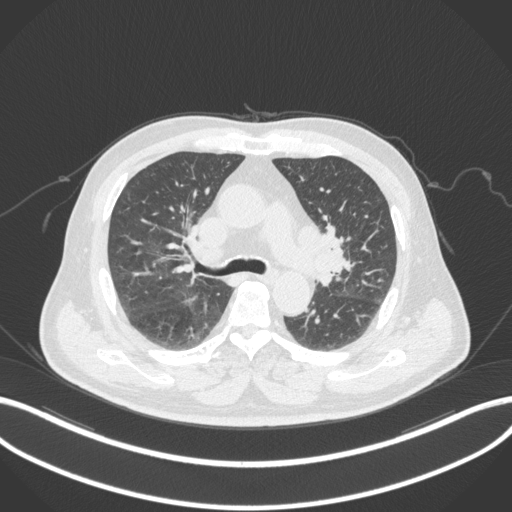
Chest CT, one axial slice; slice 188 of 286 in the series (ordered by position); reconstruction kernel B31f; 120 kVp; lung window (W 1500 / L -600 HU); 1 mm slice thickness; 512 × 512 image matrix, field of view 400 × 400 mm. Male patient, age 67 years. Case-level facts recorded for this patient, not image findings: clinical TNM (as recorded): T2a N1 M0; histopathological grade: G3.
Annotated regions visible in this slice (rectangle marked by the reading radiologist):
- lung tumour (recorded histology: adenocarcinoma): bounding box <313,226,353,275> (left, top, right, bottom; pixels)